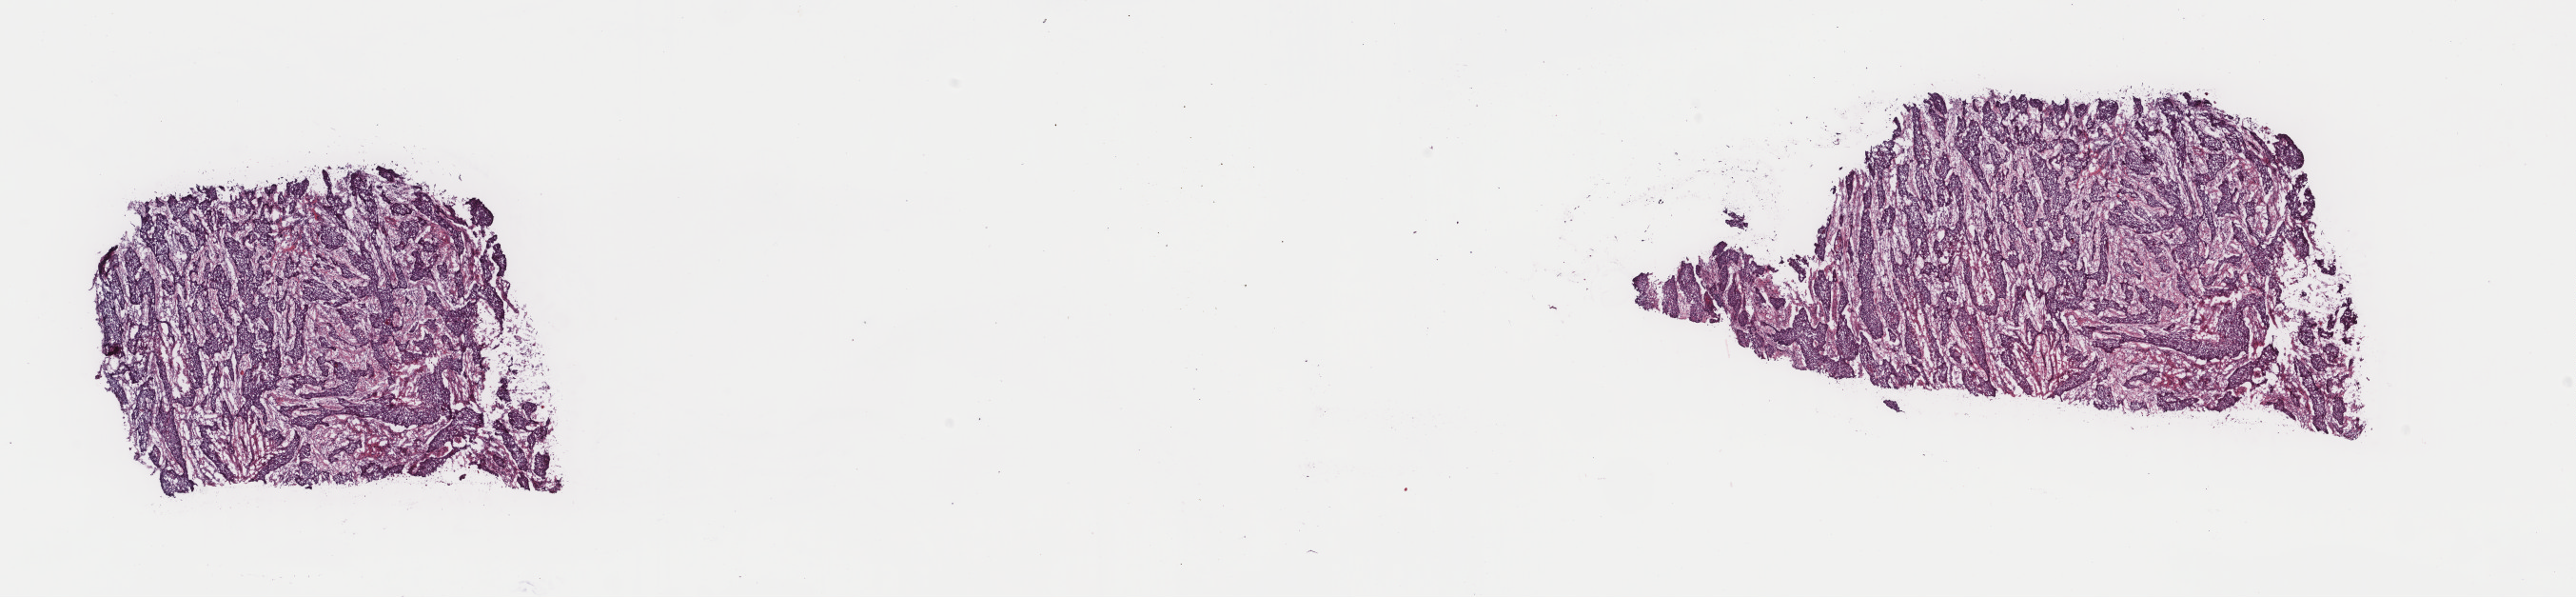
H&E-stained whole-slide image, whole scanned area (about 21.5 x 5.0 mm) shown as a low-resolution overview, frozen section from the top of the tissue portion, esophagus, primary tumour sample. Male patient; age at initial diagnosis 65 years. Histologic grade: G2 (moderately differentiated). Slide review estimates, as recorded: tumour cells 65%, tumour nuclei 80%, normal cells 0%, stromal cells 30%, necrosis 5%. Infiltration values recorded for this section: lymphocyte infiltration 2%, monocyte infiltration 0%, neutrophil infiltration 0%.
Histologic diagnosis: Squamous cell carcinoma, NOS (lower third of esophagus). TNM: T2 N0 M0. AJCC pathologic stage: II.